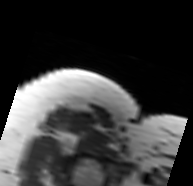
MRI of an extremity soft-tissue mass, one axial slice; slice 70 of 91 in the series (ordered by position); MR volume resampled by the dataset authors to the PET/CT grid (not the native acquisition matrix); 3.27 mm slice thickness; 193 × 186 image matrix. Female patient. Case-level facts recorded for this patient, not image findings: histological type: malignant solitary fibrous tumor; grade: intermediate; site of the primary tumour: right thigh.
Outlined on this slice (expert contour drawn on MRI and transferred to this co-registered scan by the dataset authors):
- gross tumour volume including surrounding oedema: bounding box <60,128,86,150> (left, top, right, bottom; pixels)